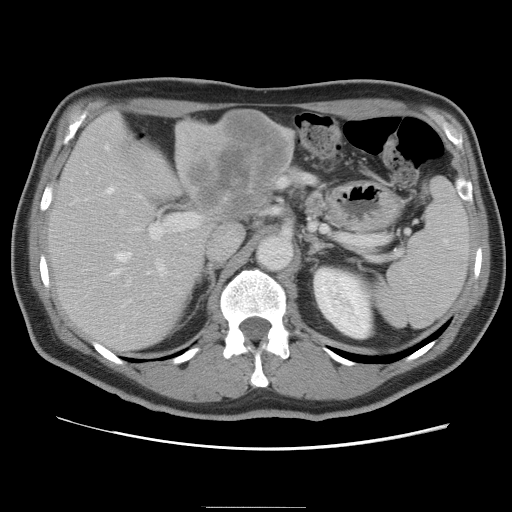
Contrast-enhanced abdominal CT, one axial slice; slice 50 of 87 in the series (ordered by position); 120 kVp; intravenous contrast given; soft-tissue window (W 400 / L 40 HU); 5 mm slice thickness; 512 × 512 image matrix, field of view 363 × 363 mm. Male patient, age 63 years. From the clinical record (not read from this slice): diagnosis: colorectal cancer liver metastases, imaged before liver resection; multiple liver metastases: no; largest metastasis: 9 cm; chemotherapy before resection: no.
Outlined on this slice (expert manual segmentation):
- hepatic veins: bounding box (x1, y1, x2, y2) in pixels: (103, 146, 151, 307)
- liver: (48, 111, 295, 355)
- planned liver remnant (the part of the liver to remain after resection): (49, 146, 205, 355)
- portal vein (with intrahepatic branches): (120, 210, 204, 287)
- liver metastasis: (188, 117, 290, 220)